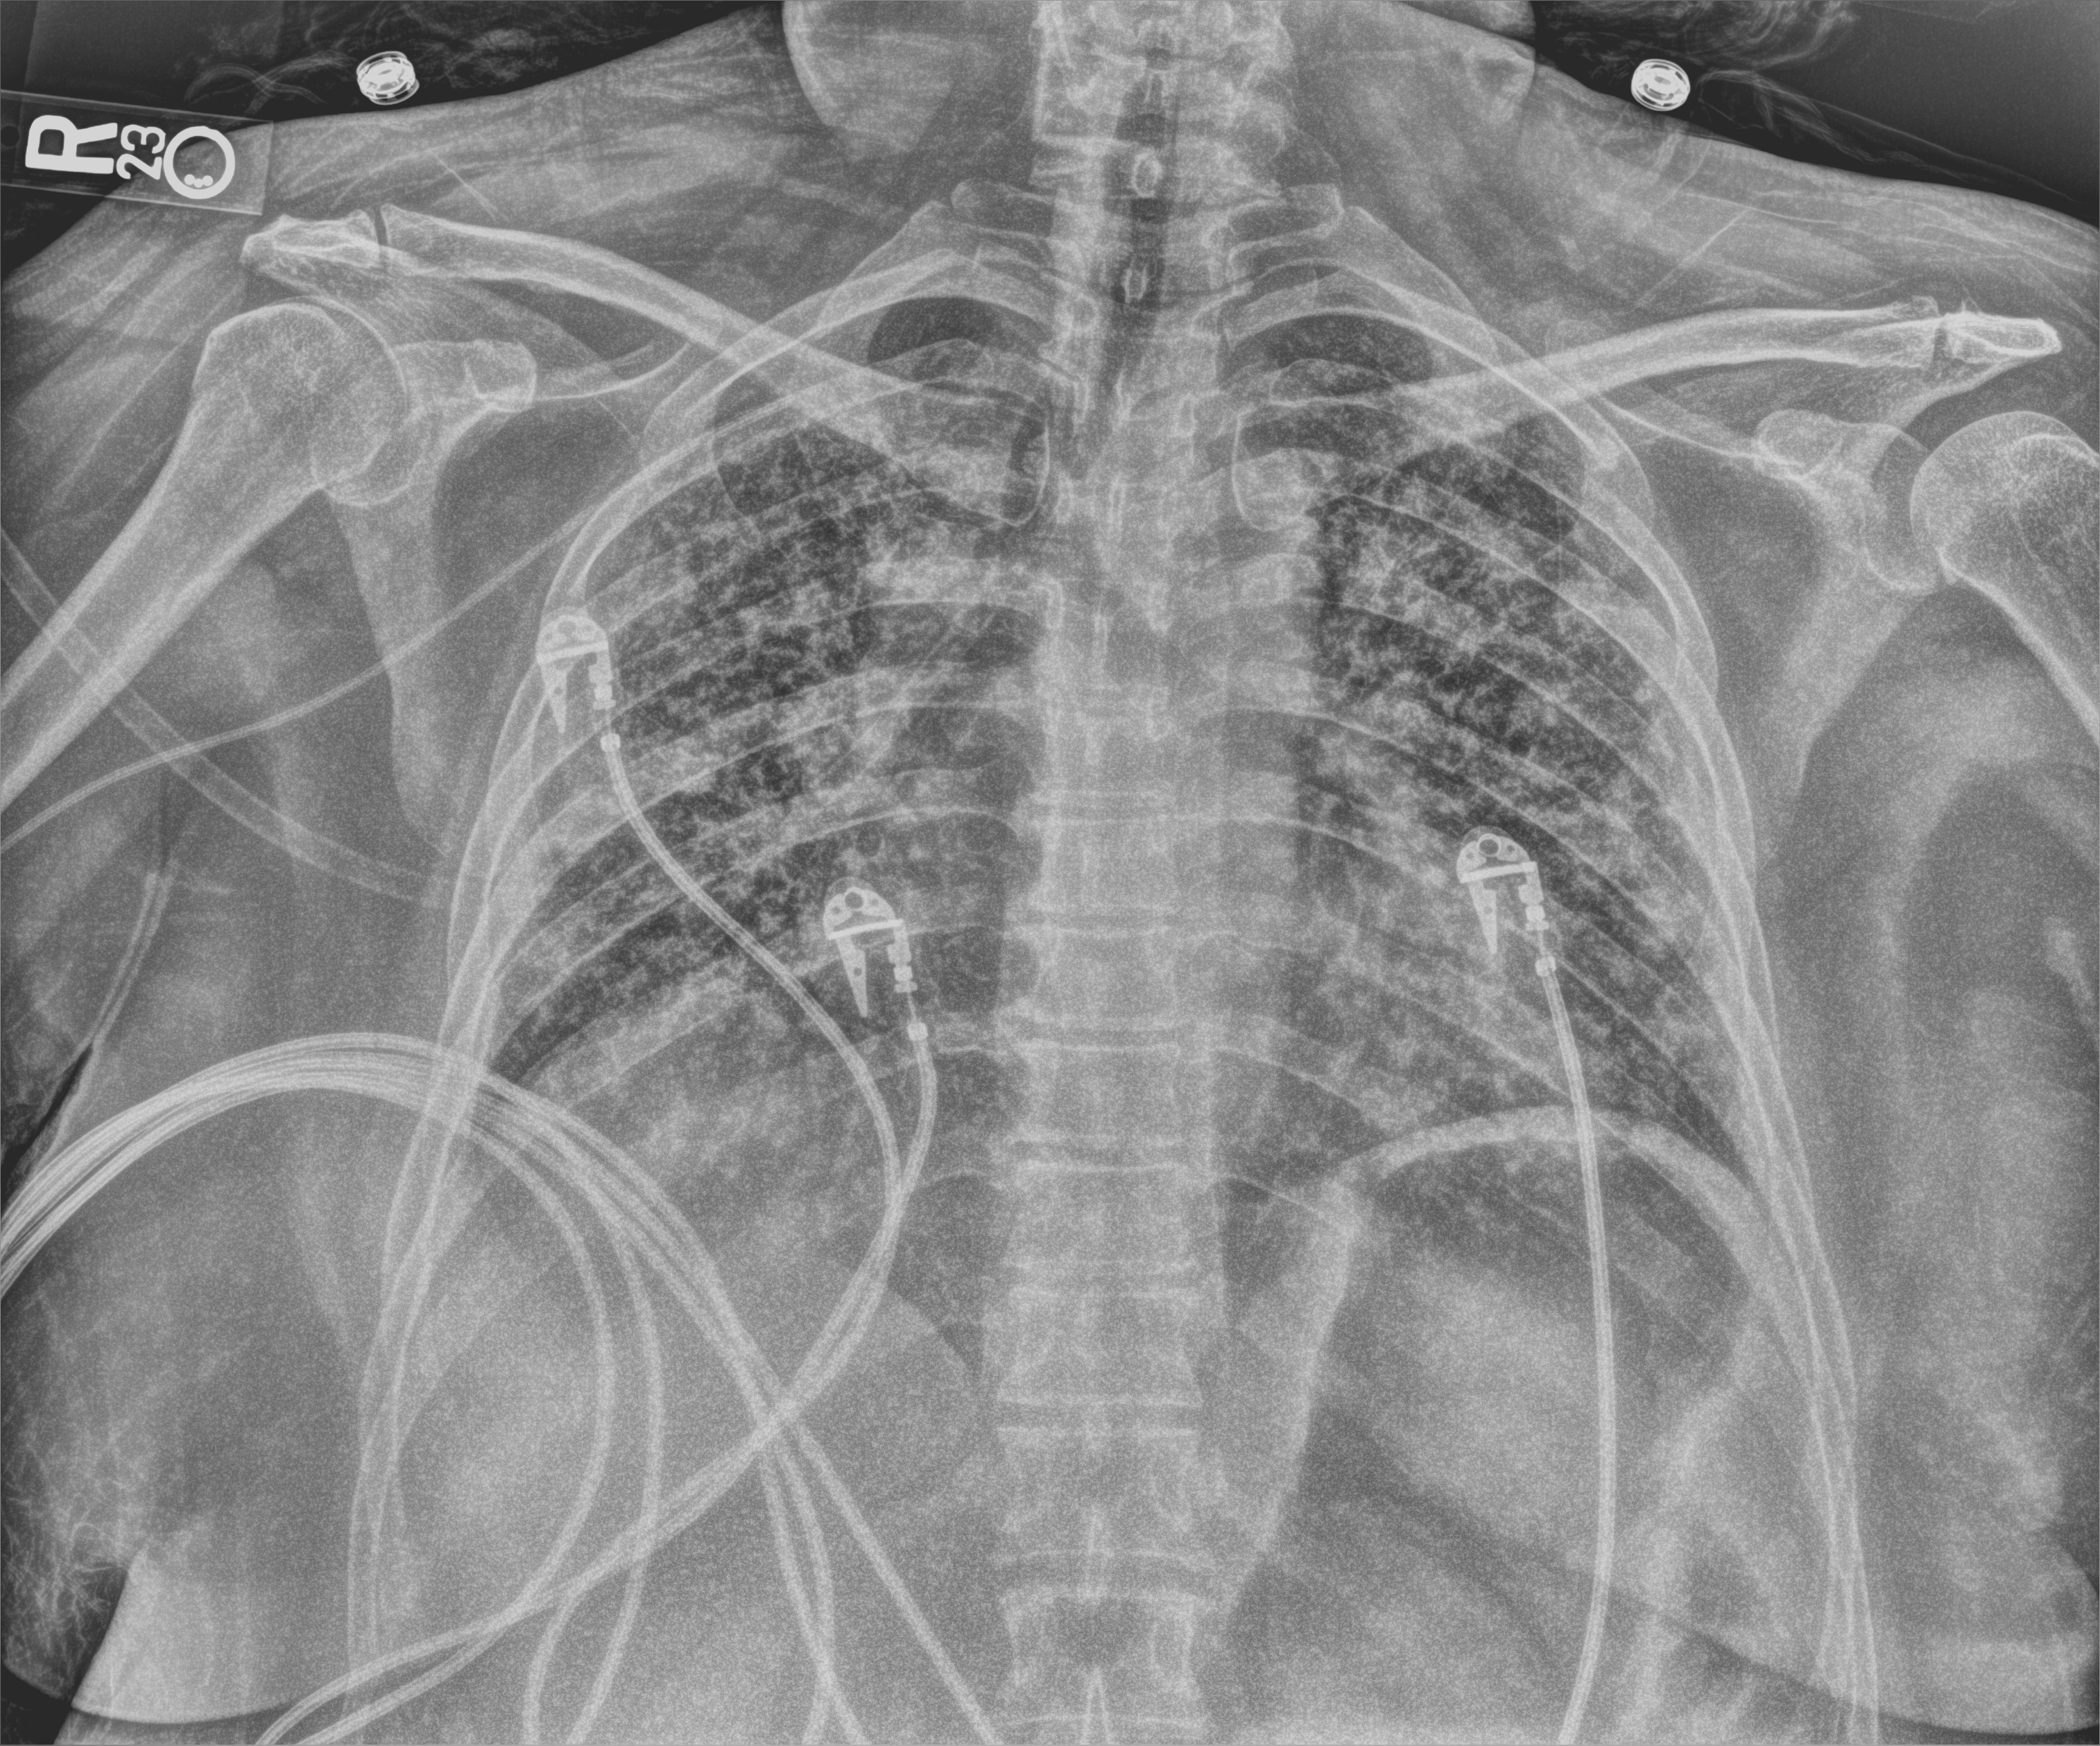
Bedside chest radiograph (computed radiography), anteroposterior (AP) projection. Patient hospitalised with COVID-19; female, aged 18–59 years.
From the hospital-stay record, not from the radiograph (when in the stay this image was taken is not recorded): admitted to intensive care during this hospital stay: no.